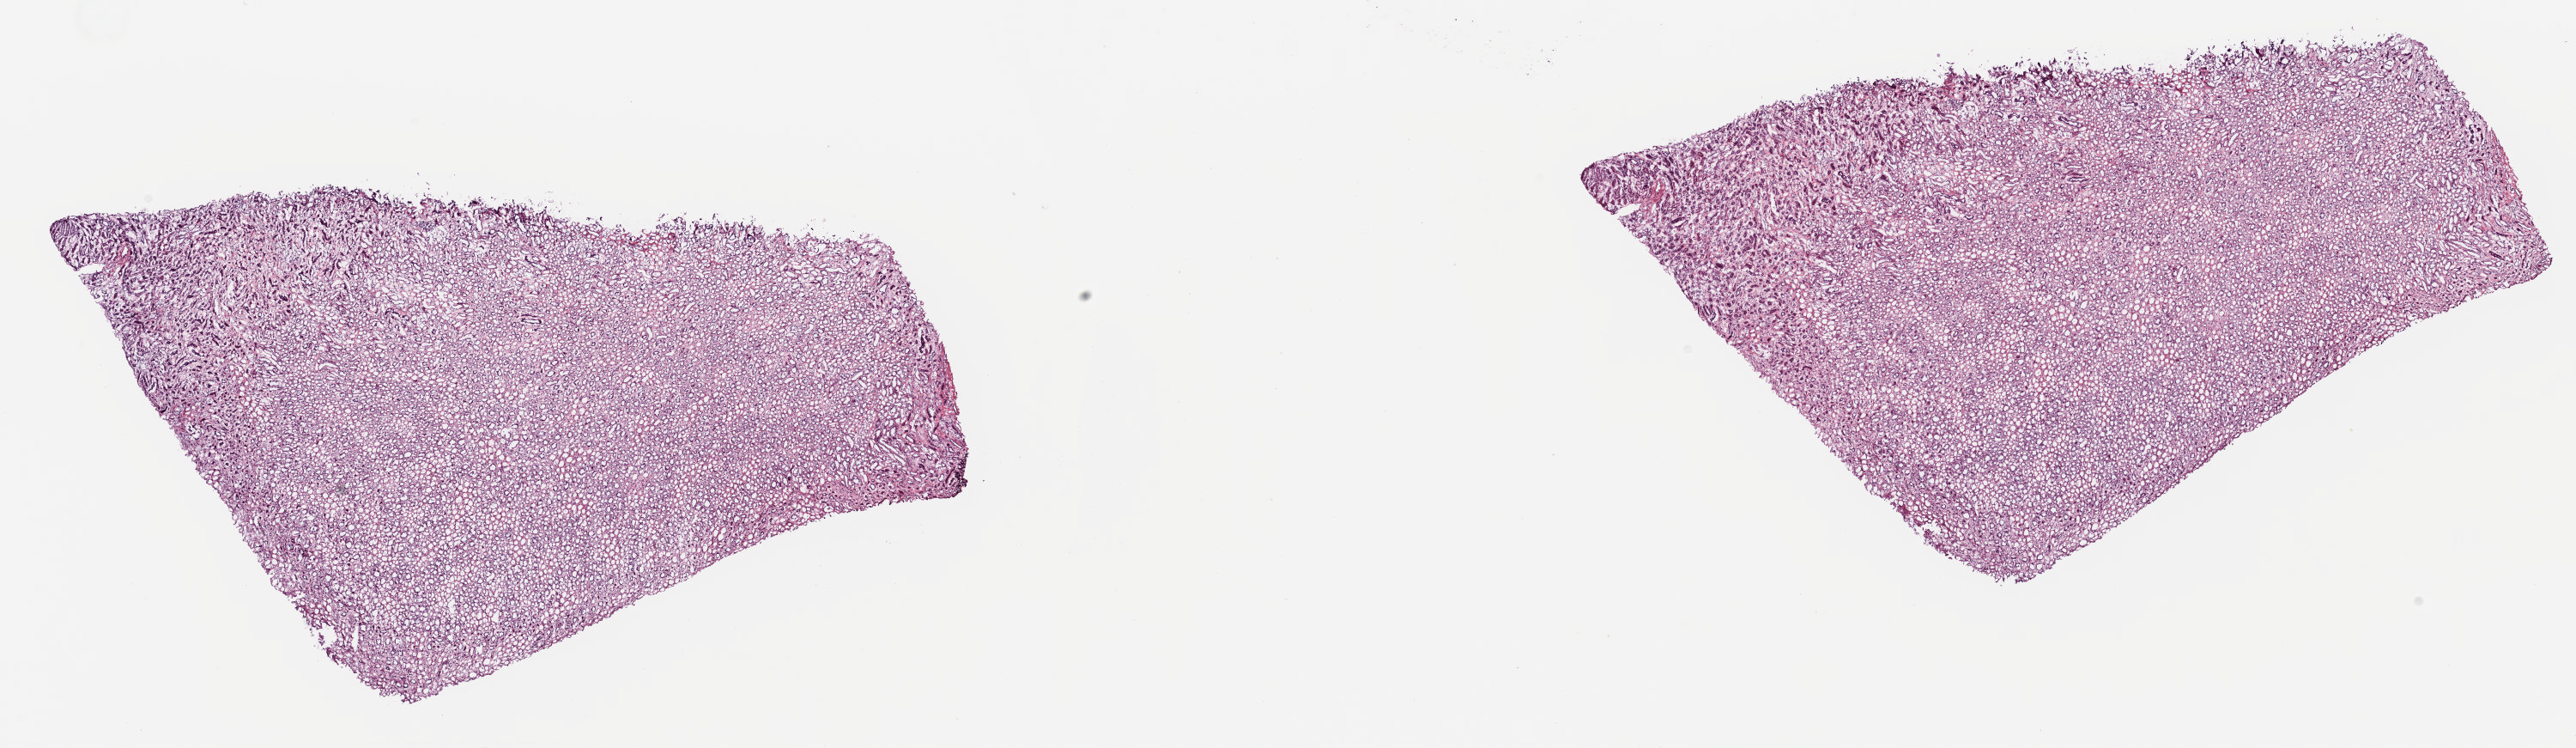
Digitized H&E-stained tissue section (whole slide) — whole scanned area (about 23.8 x 6.9 mm, from a 20x scan) shown as a low-resolution overview. Frozen section. Retroperitoneum and peritoneum, solid tissue normal (non-tumour tissue) sample. Female, age 44 years at initial diagnosis. Pathologist review of this section (percent, as recorded): tumour cells 0%, tumour nuclei 0%, normal cells 100%, stromal cells 0%, necrosis 0%. Inflammatory infiltration, as recorded: lymphocyte infiltration 1%, monocyte infiltration 0%, neutrophil infiltration 0%.
This section: solid tissue normal (non-tumour) sample from the same patient. Patient diagnosis: Dedifferentiated liposarcoma (retroperitoneum).